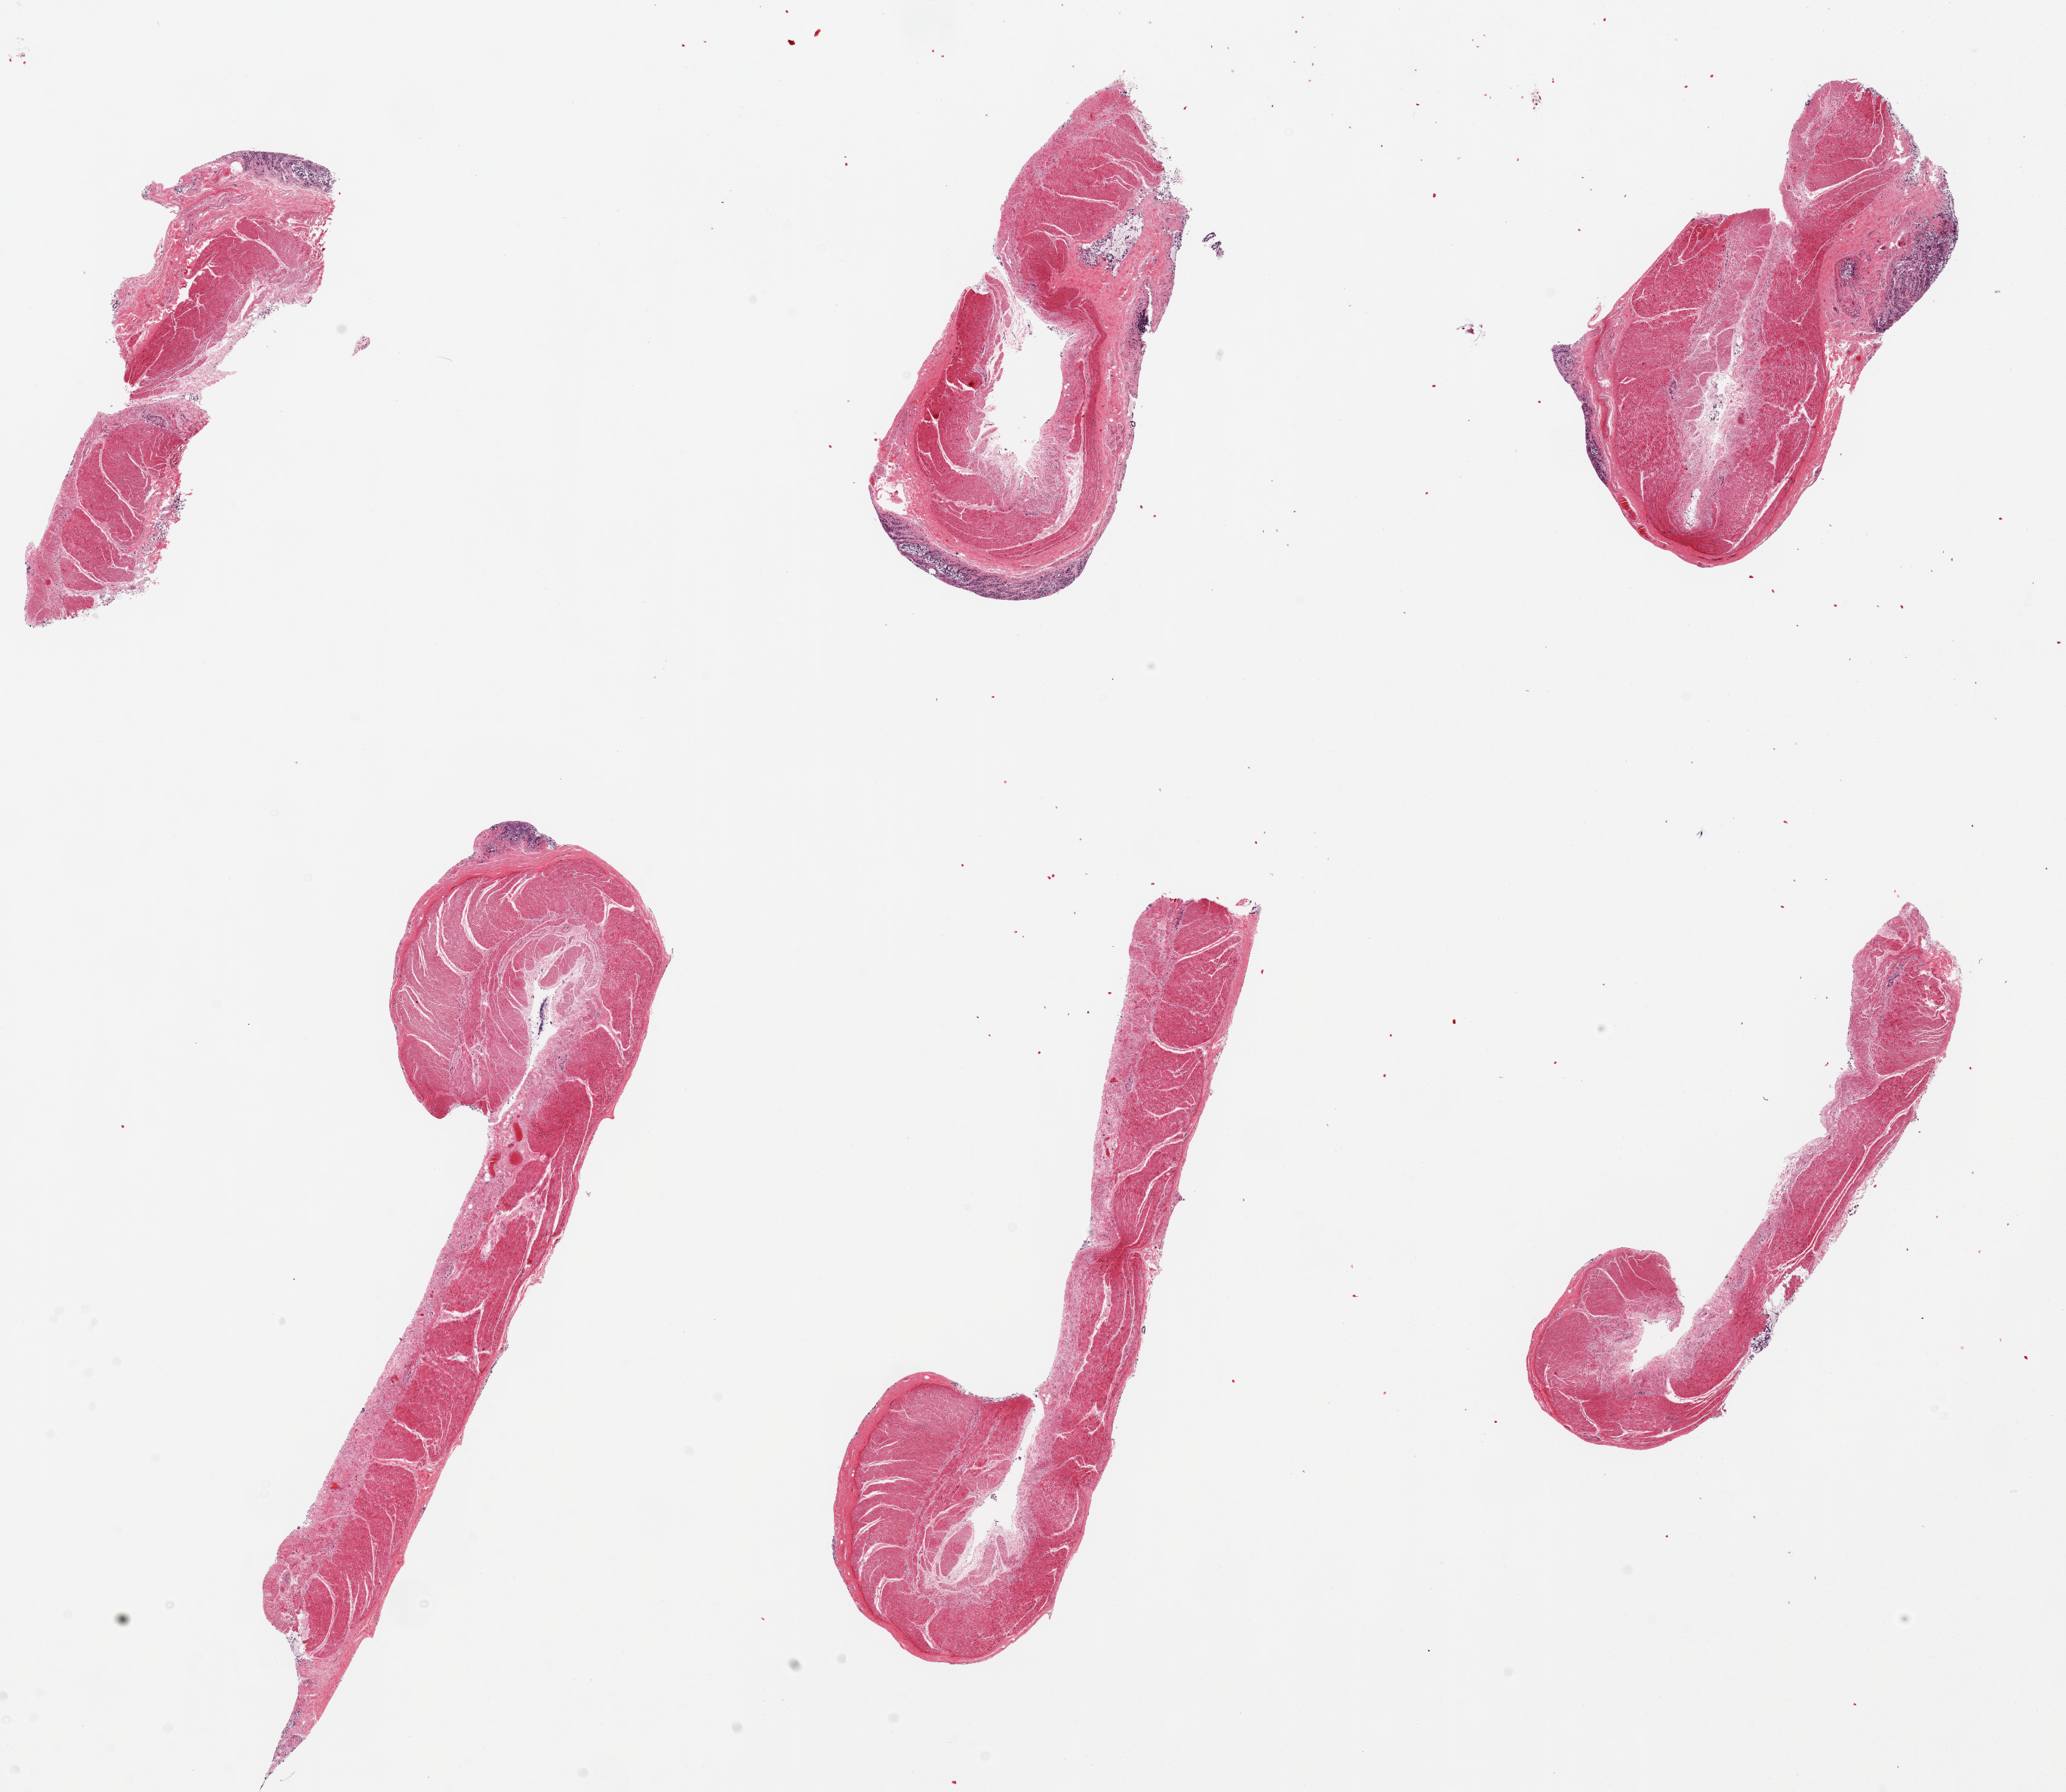
Digitized H&E-stained section, brightfield — shown as a low-resolution overview of the whole scanned area (about 21.7 x 18.8 mm), PAXgene-fixed paraffin-embedded (PFPE) section, sampled site (target tissue): sigmoid colon, tissue donor sample.
Reviewer comment on this tissue sample: 6 pieces trace amounts autolyzed mucosa lamina propria elements only.